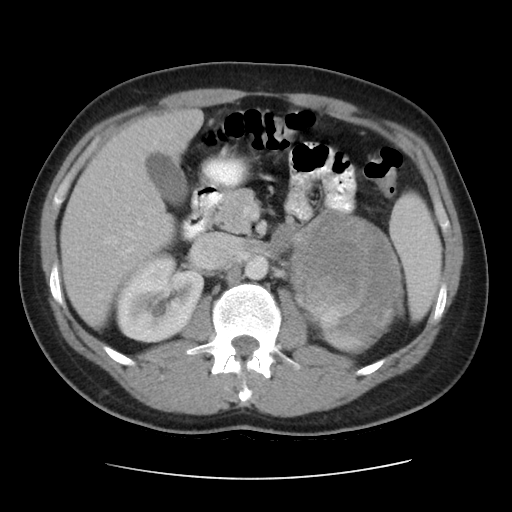
Contrast-enhanced abdominal CT, one axial slice. Slice 24 of 48 in the series (ordered by position). 120 kVp. Intravenous contrast given. Soft-tissue window (W 400 / L 40 HU). 512 × 512 image matrix, field of view 360 × 360 mm. Patient: male, 32 years. From the clinical record (not read from this slice): diagnosis: adrenocortical carcinoma; tumour side: left adrenal; tumour size at pathology: 14 cm; Ki-67 index: 67 %; stage (as recorded): 3.
Structures marked on this image (semi-automatically segmented with operator editing):
- mass: bounding box <294,213,401,350> (left, top, right, bottom; pixels)